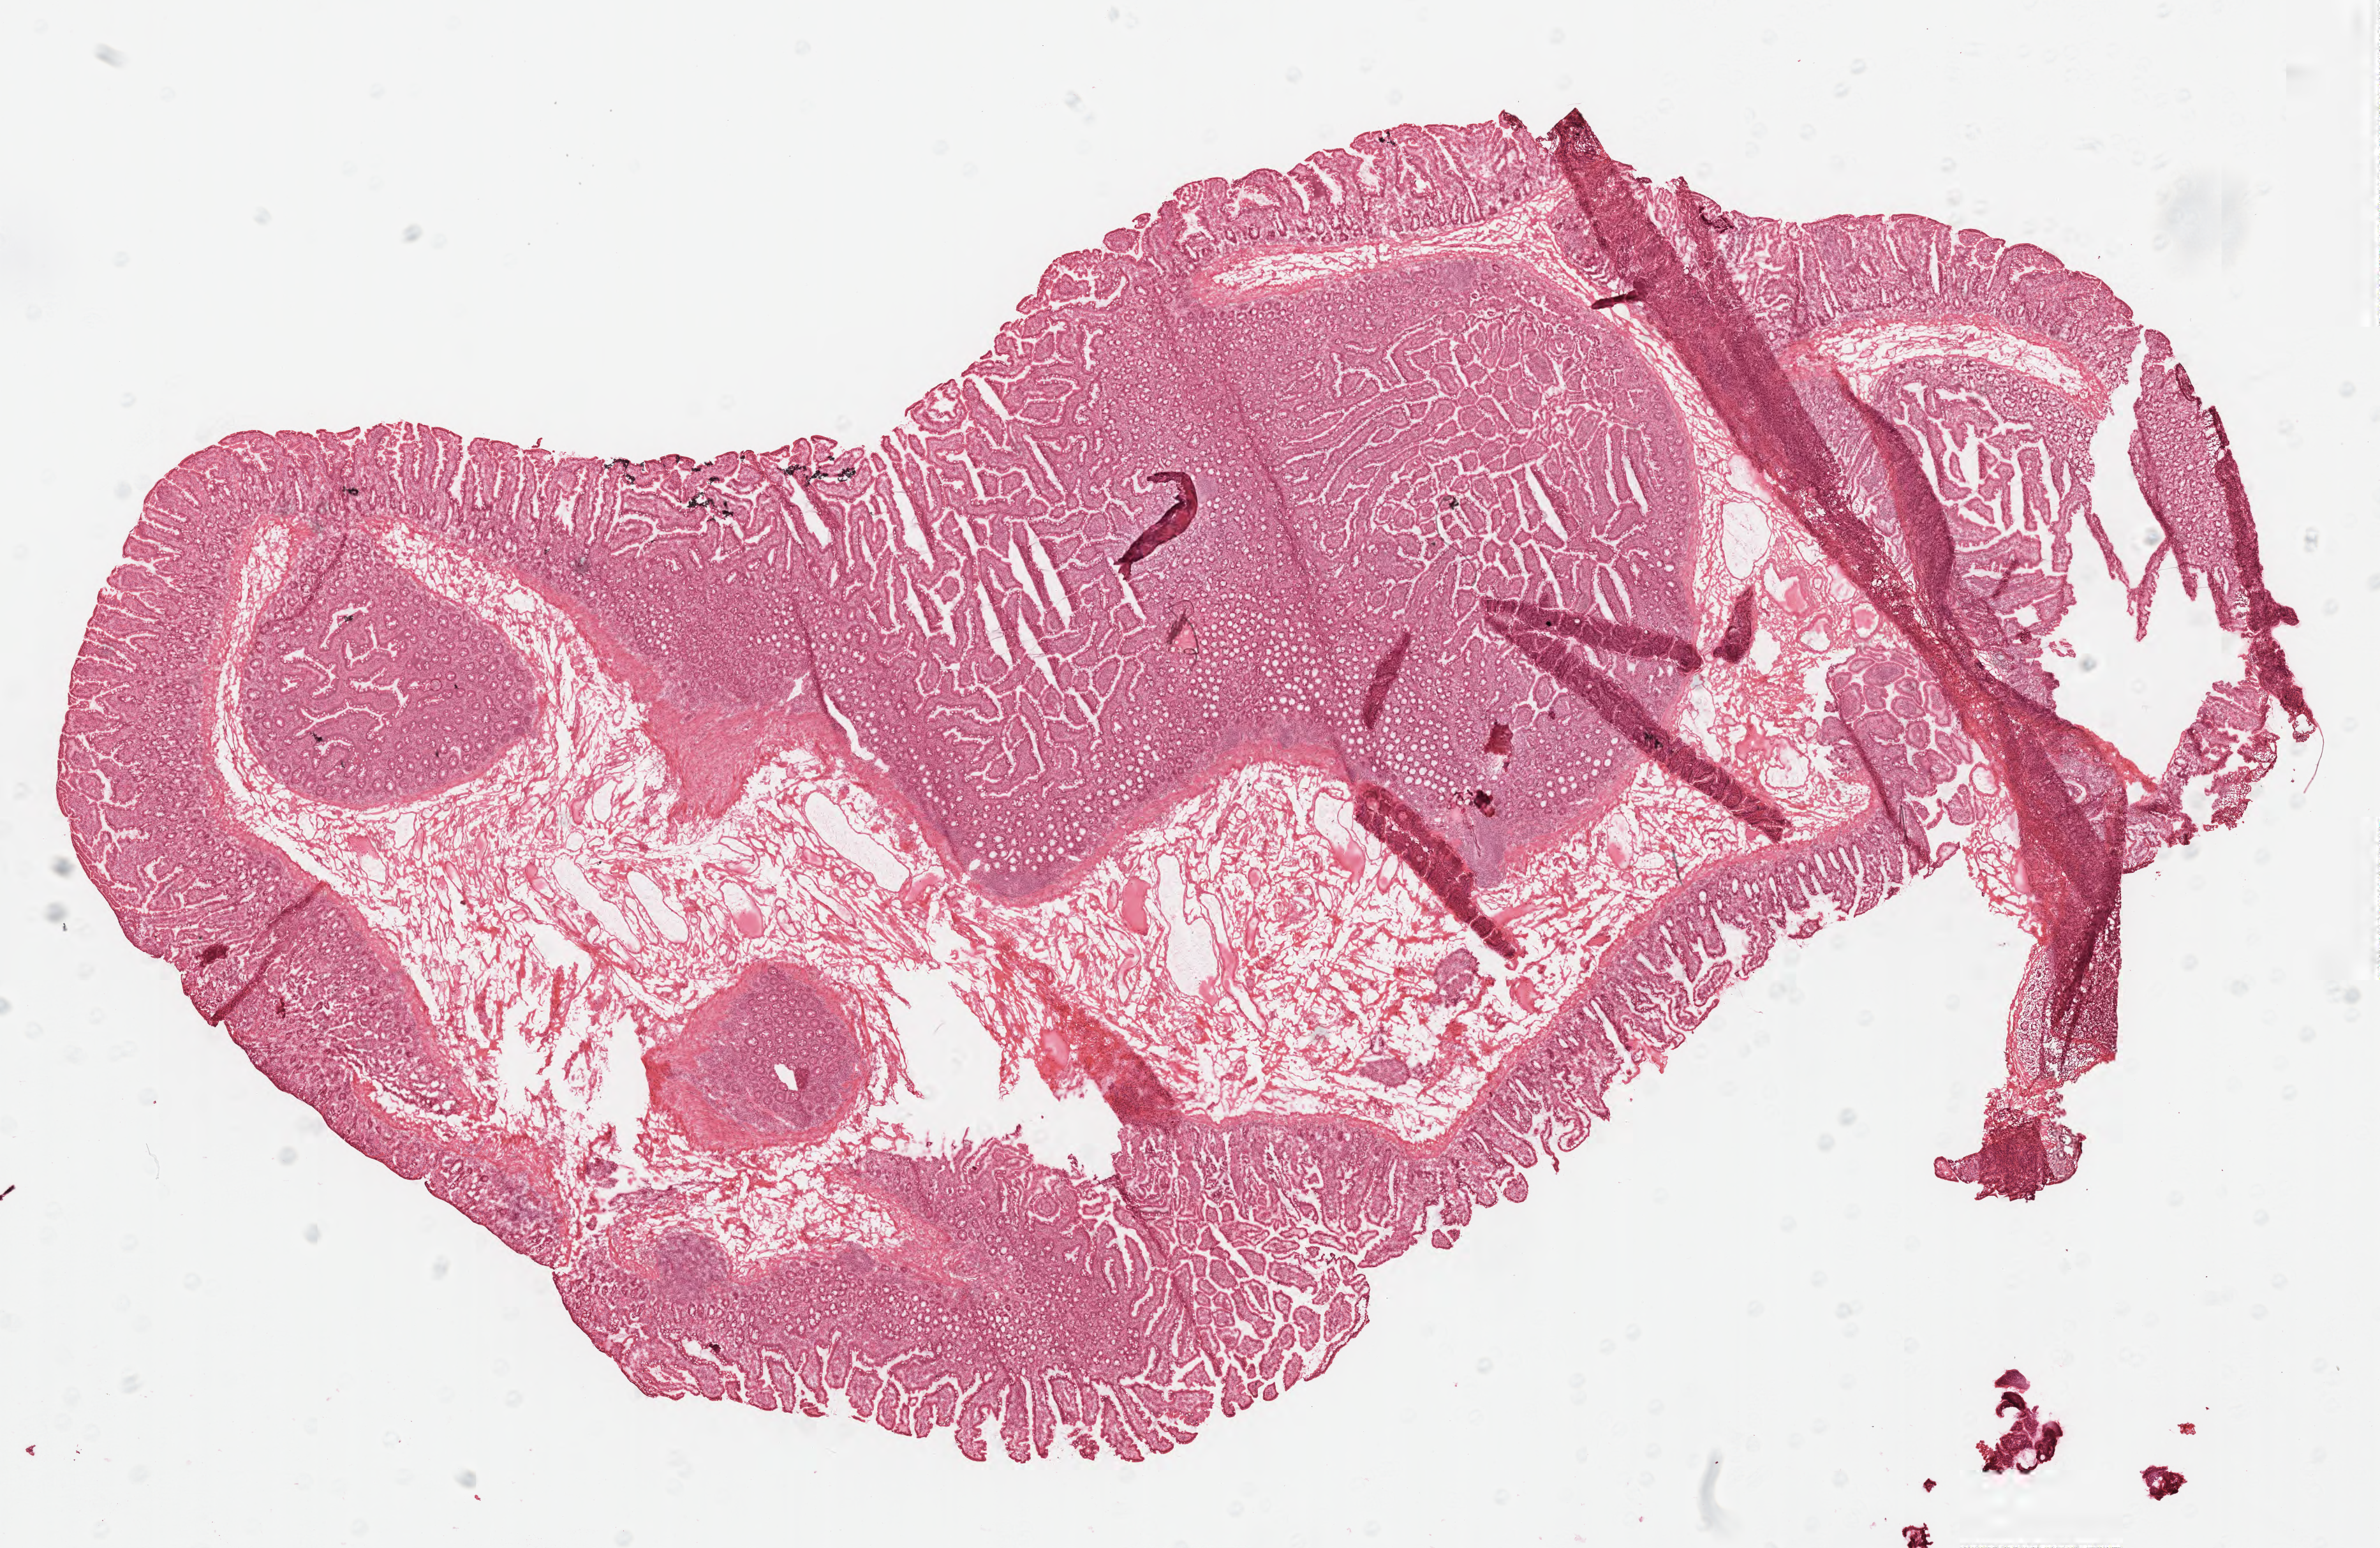
Haematoxylin and eosin whole-slide image — shown as a low-resolution overview of the whole scanned area (about 14.7 x 9.6 mm); frozen section (tissue freezing medium); specimen: non-tumor (normal tissue) sample from a patient with infiltrating duct carcinoma, NOS; site: head of pancreas. Patient: male, age at initial diagnosis 75 years. Pathologist review of this section (percent, as recorded): tumor cells 0%, tumor nuclei 0%, stromal cells 0%, necrosis 0%, normal cells 100%. Inflammatory infiltration, as recorded: lymphocyte infiltration 0%, monocyte infiltration 0%, neutrophil infiltration 0%.
• this section: non-tumor tissue sample; the patient's diagnosis is given above
• section: top of the tissue portion